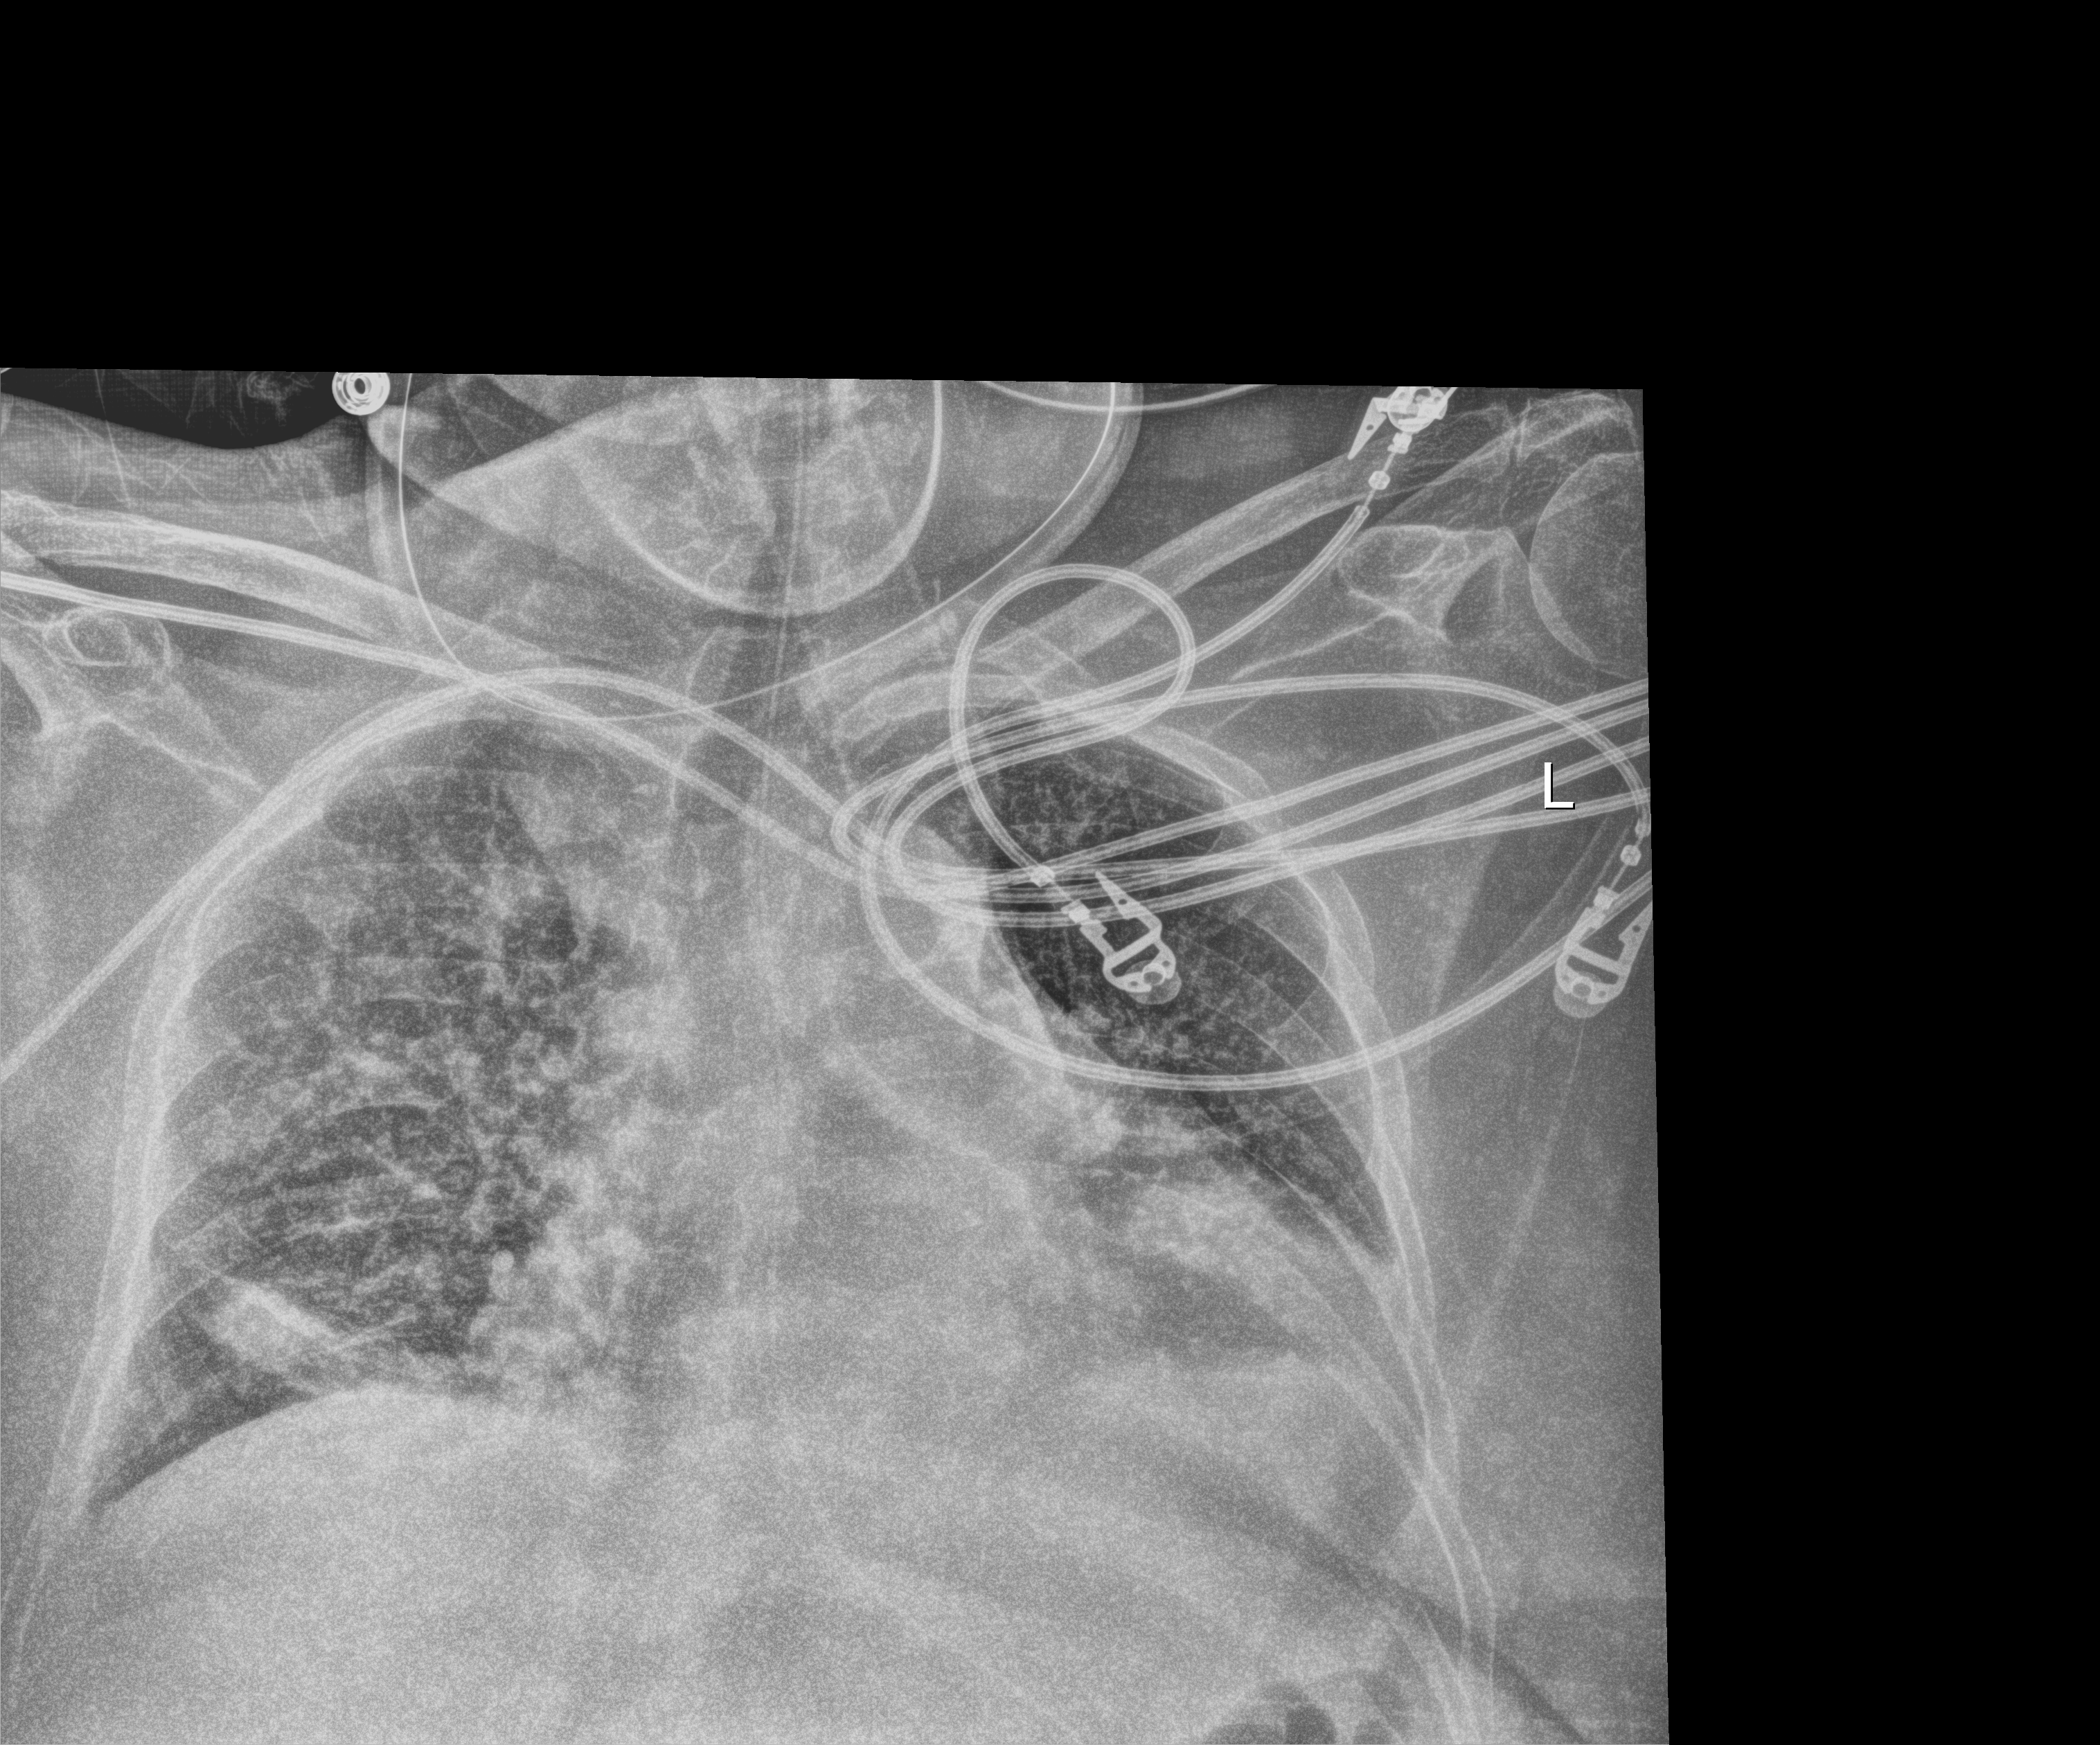
Bedside chest radiograph (digital radiography). Patient hospitalised with COVID-19; female, aged 60–74 years.
Hospital-stay facts (about this admission, not read from this image; timing relative to this image not recorded):
- mechanically ventilated during this hospital stay: no
- admitted to intensive care during this hospital stay: yes